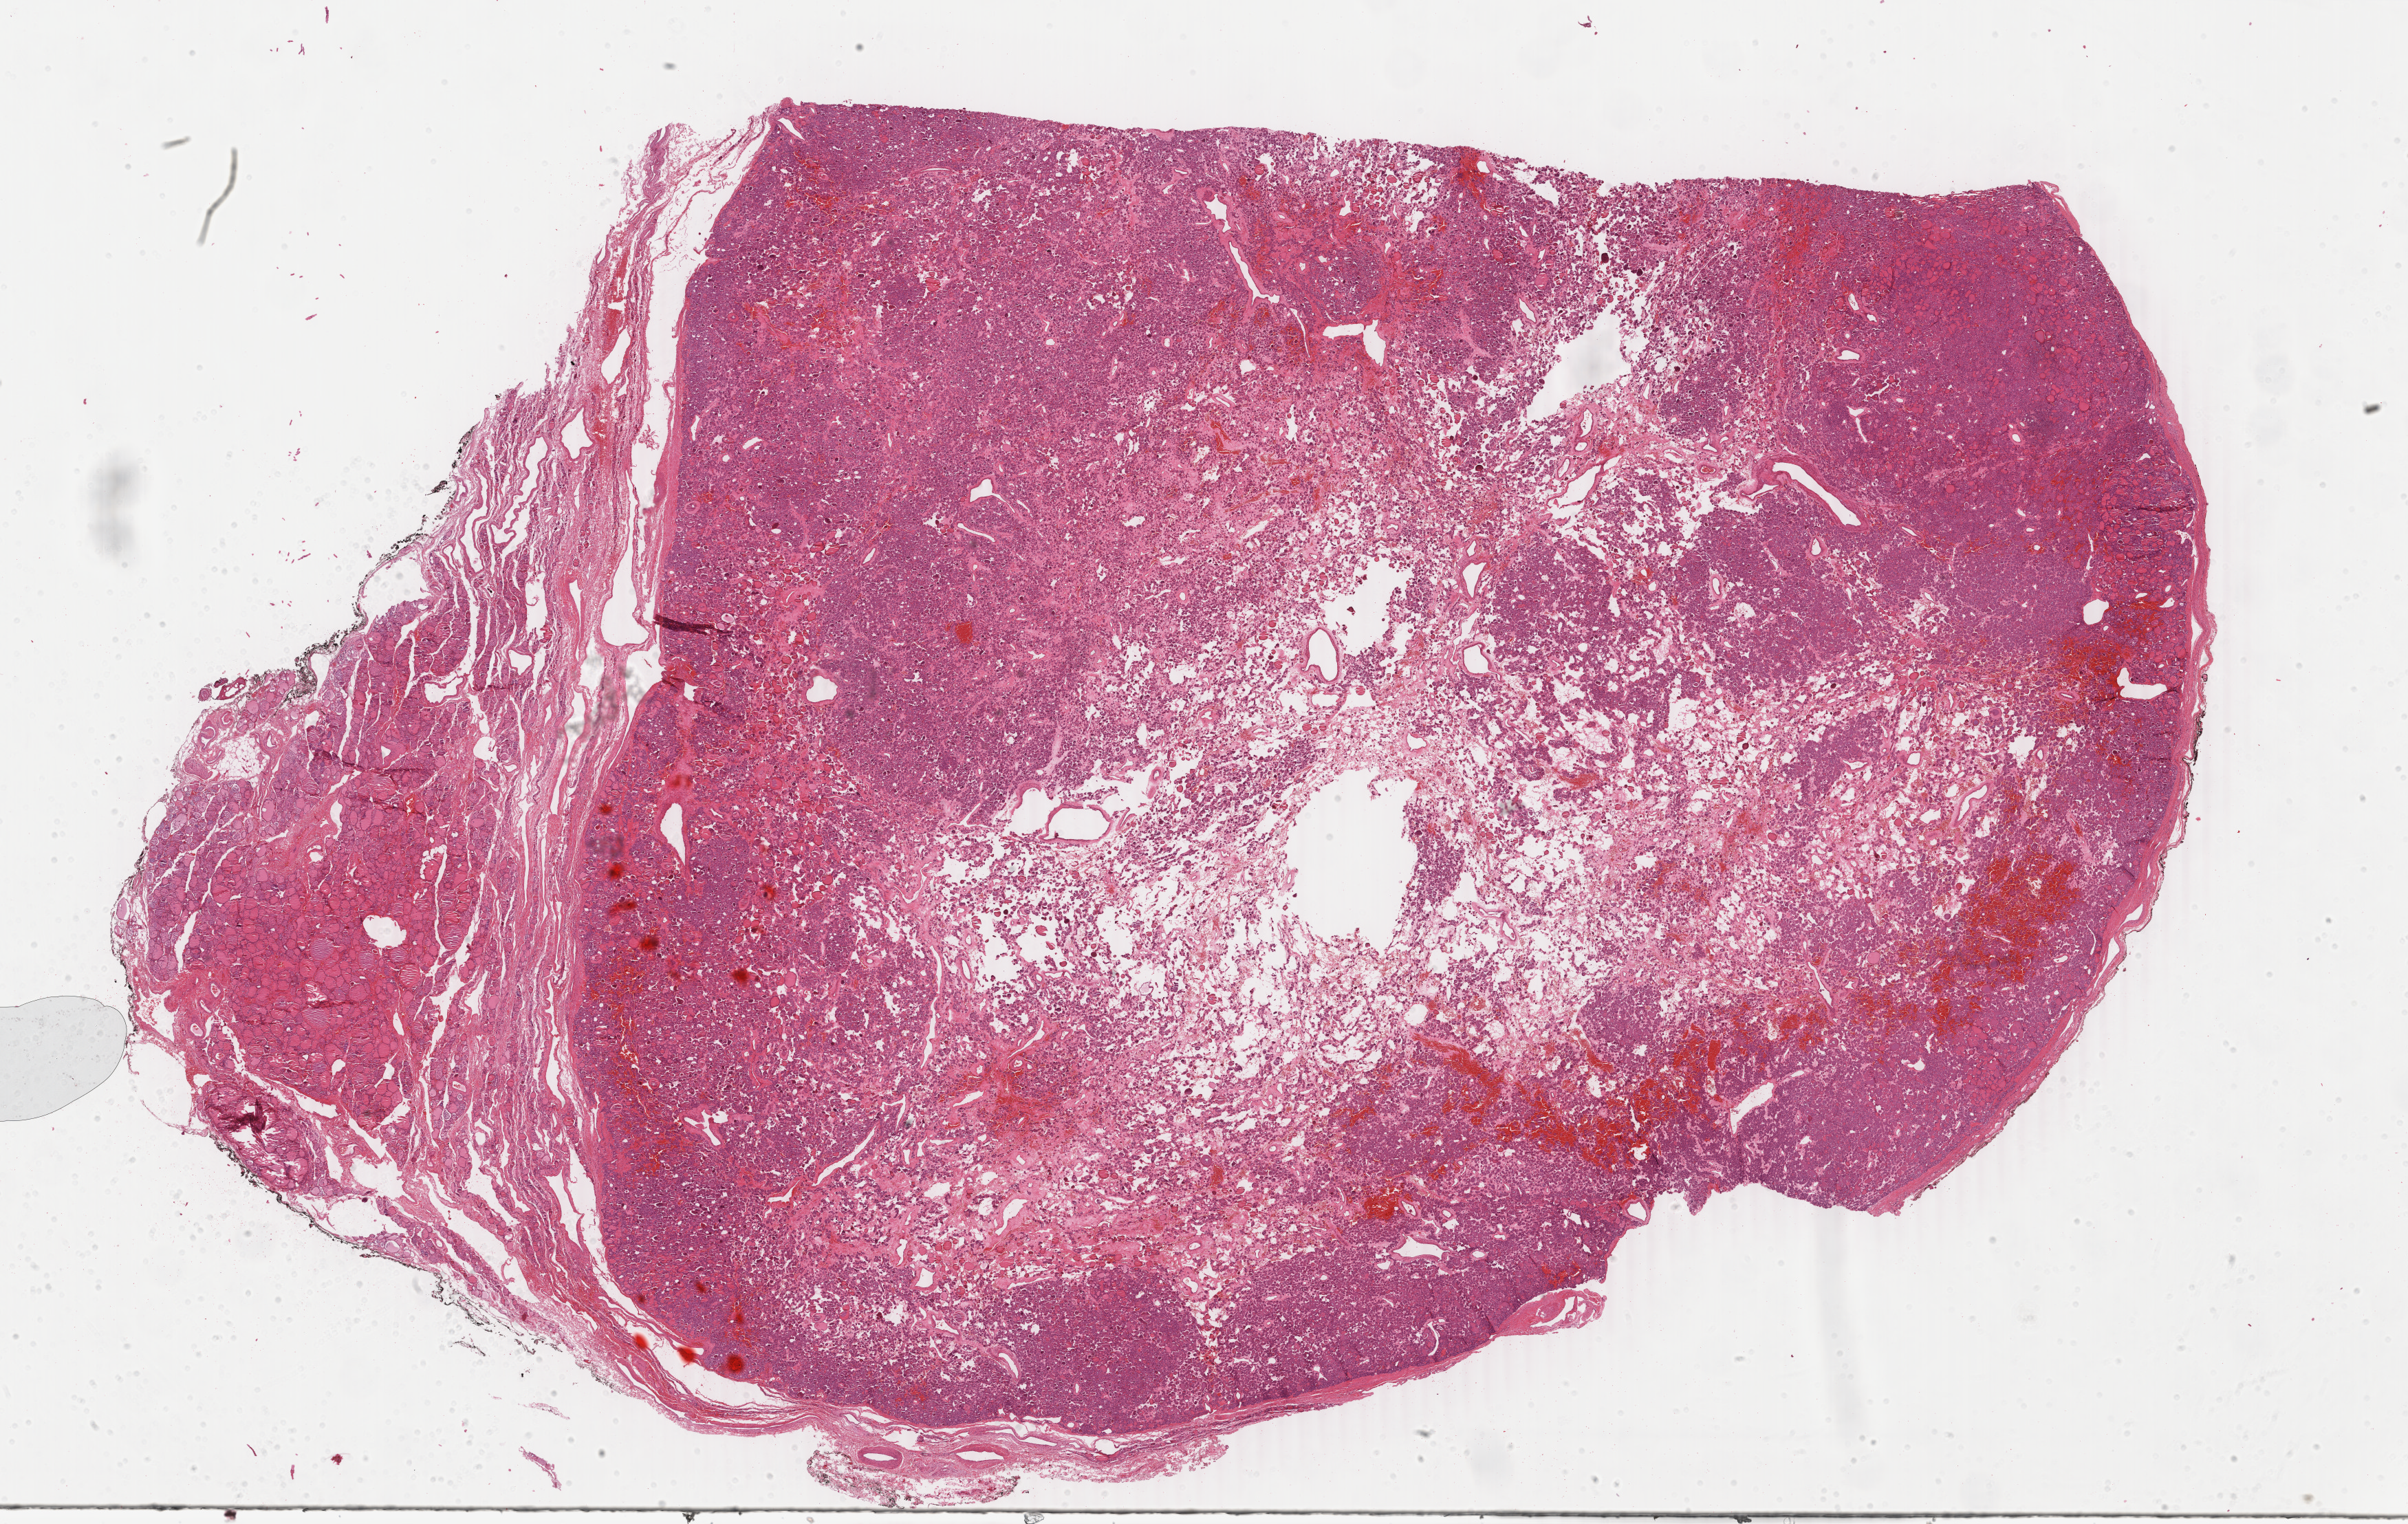
Whole-slide histology image, H&E, low-resolution overview of the scanned area, about 27.8 x 17.6 mm (acquisition: 40x scan). Formalin-fixed paraffin-embedded (FFPE) diagnostic section. Primary tumour sample from the thyroid. Male patient; age at initial diagnosis 79 years.
Pathologic diagnosis: Papillary adenocarcinoma, NOS. AJCC pathologic stage: II.